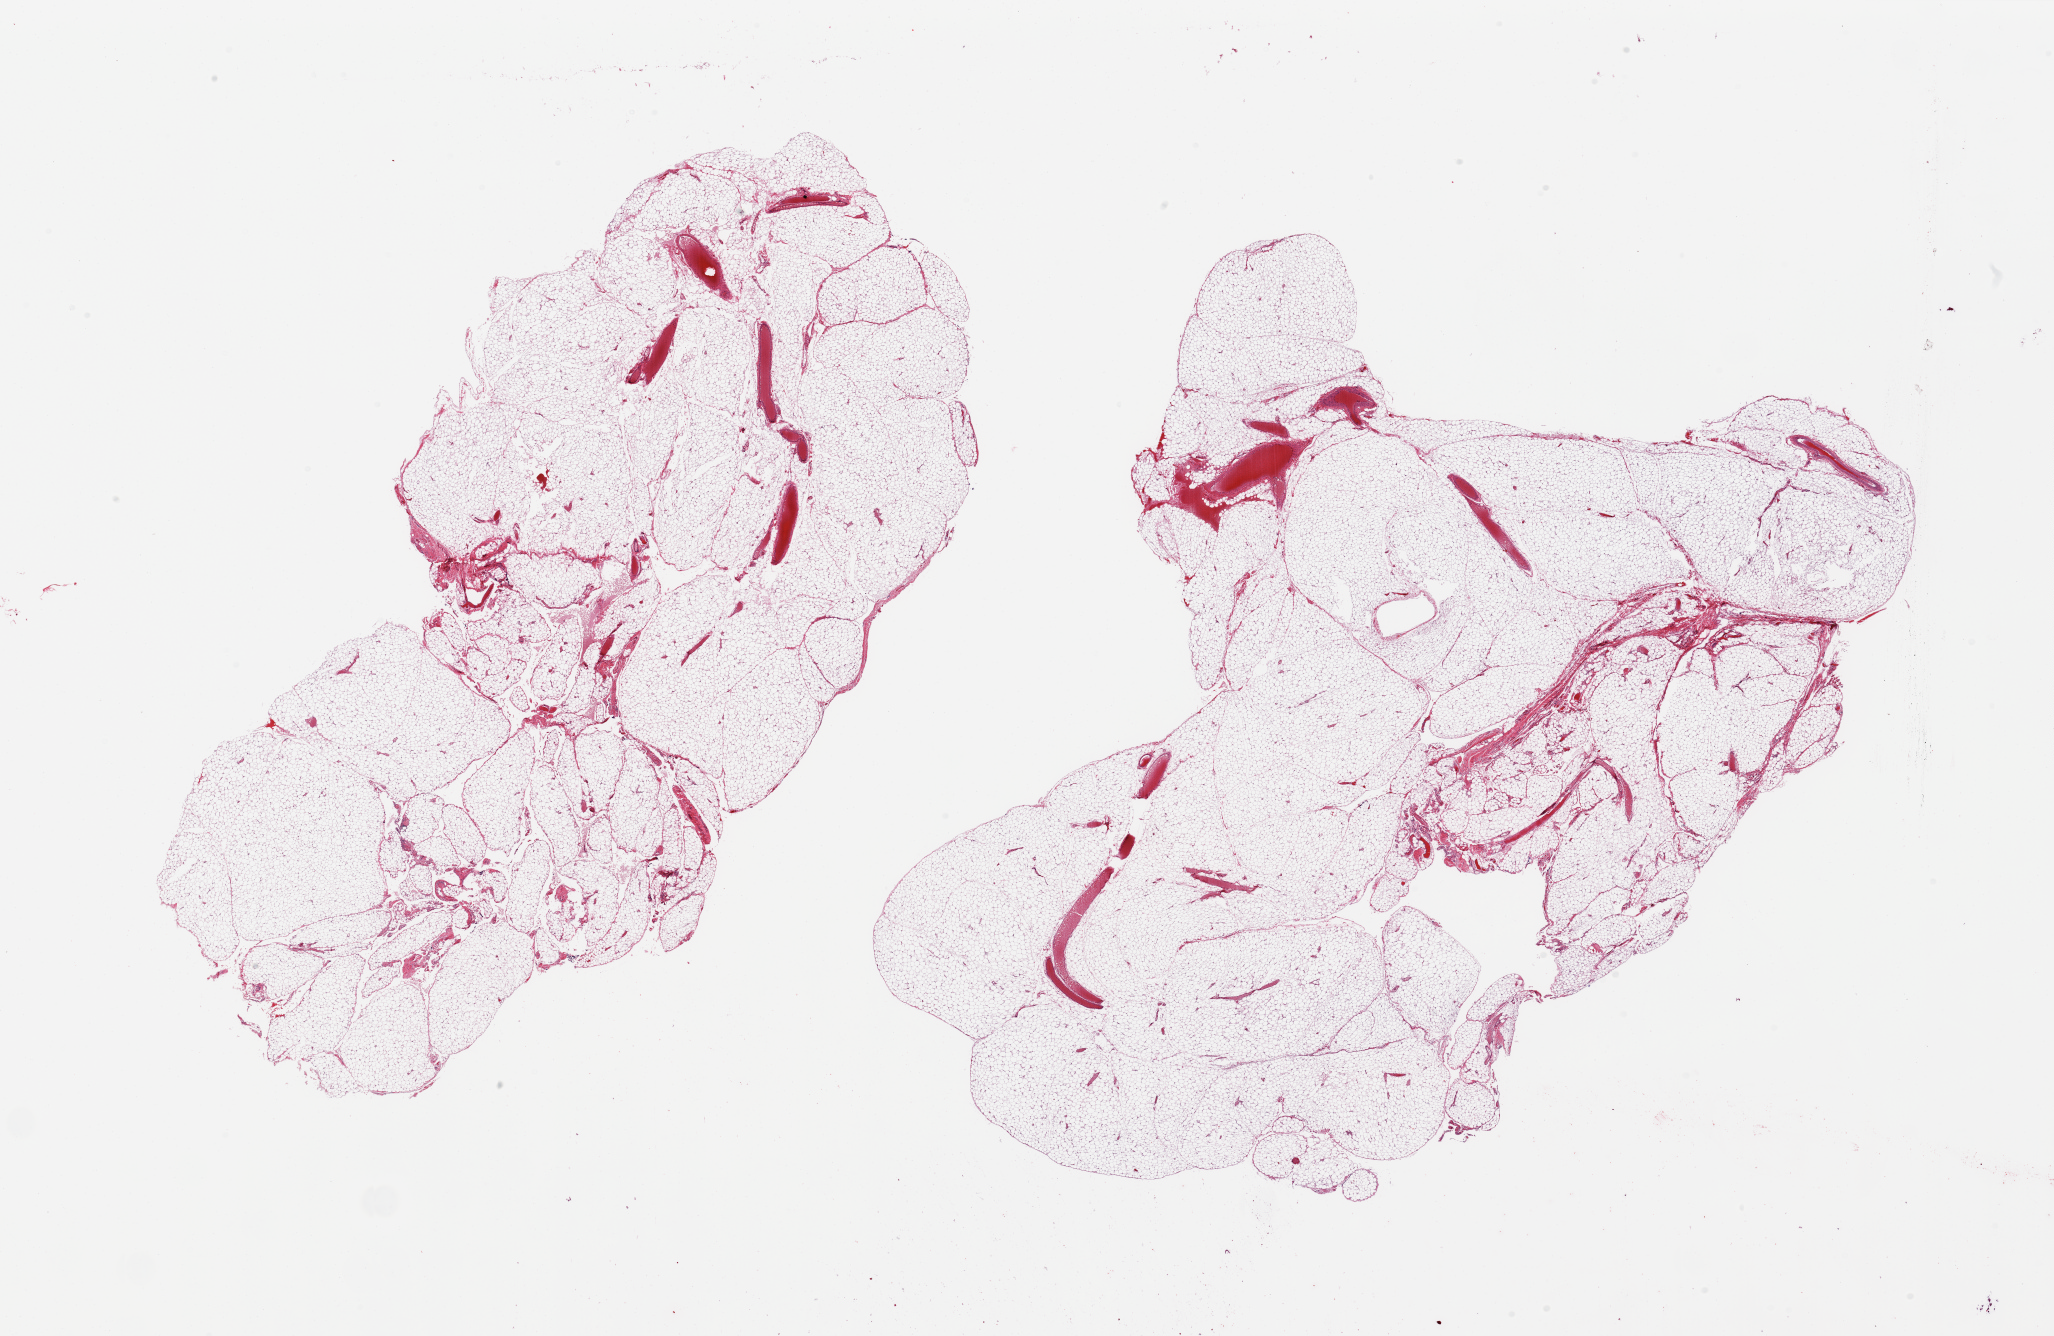
Digitized haematoxylin and eosin-stained section — low-resolution overview of the scanned area, about 32.5 x 21.1 mm. PAXgene-fixed, paraffin-embedded tissue. Target tissue: omentum. Tissue donor sample. Donor: male.
* reviewer comment on this tissue sample: 2 pieces; lobulated mature fat, includes few larger vessels